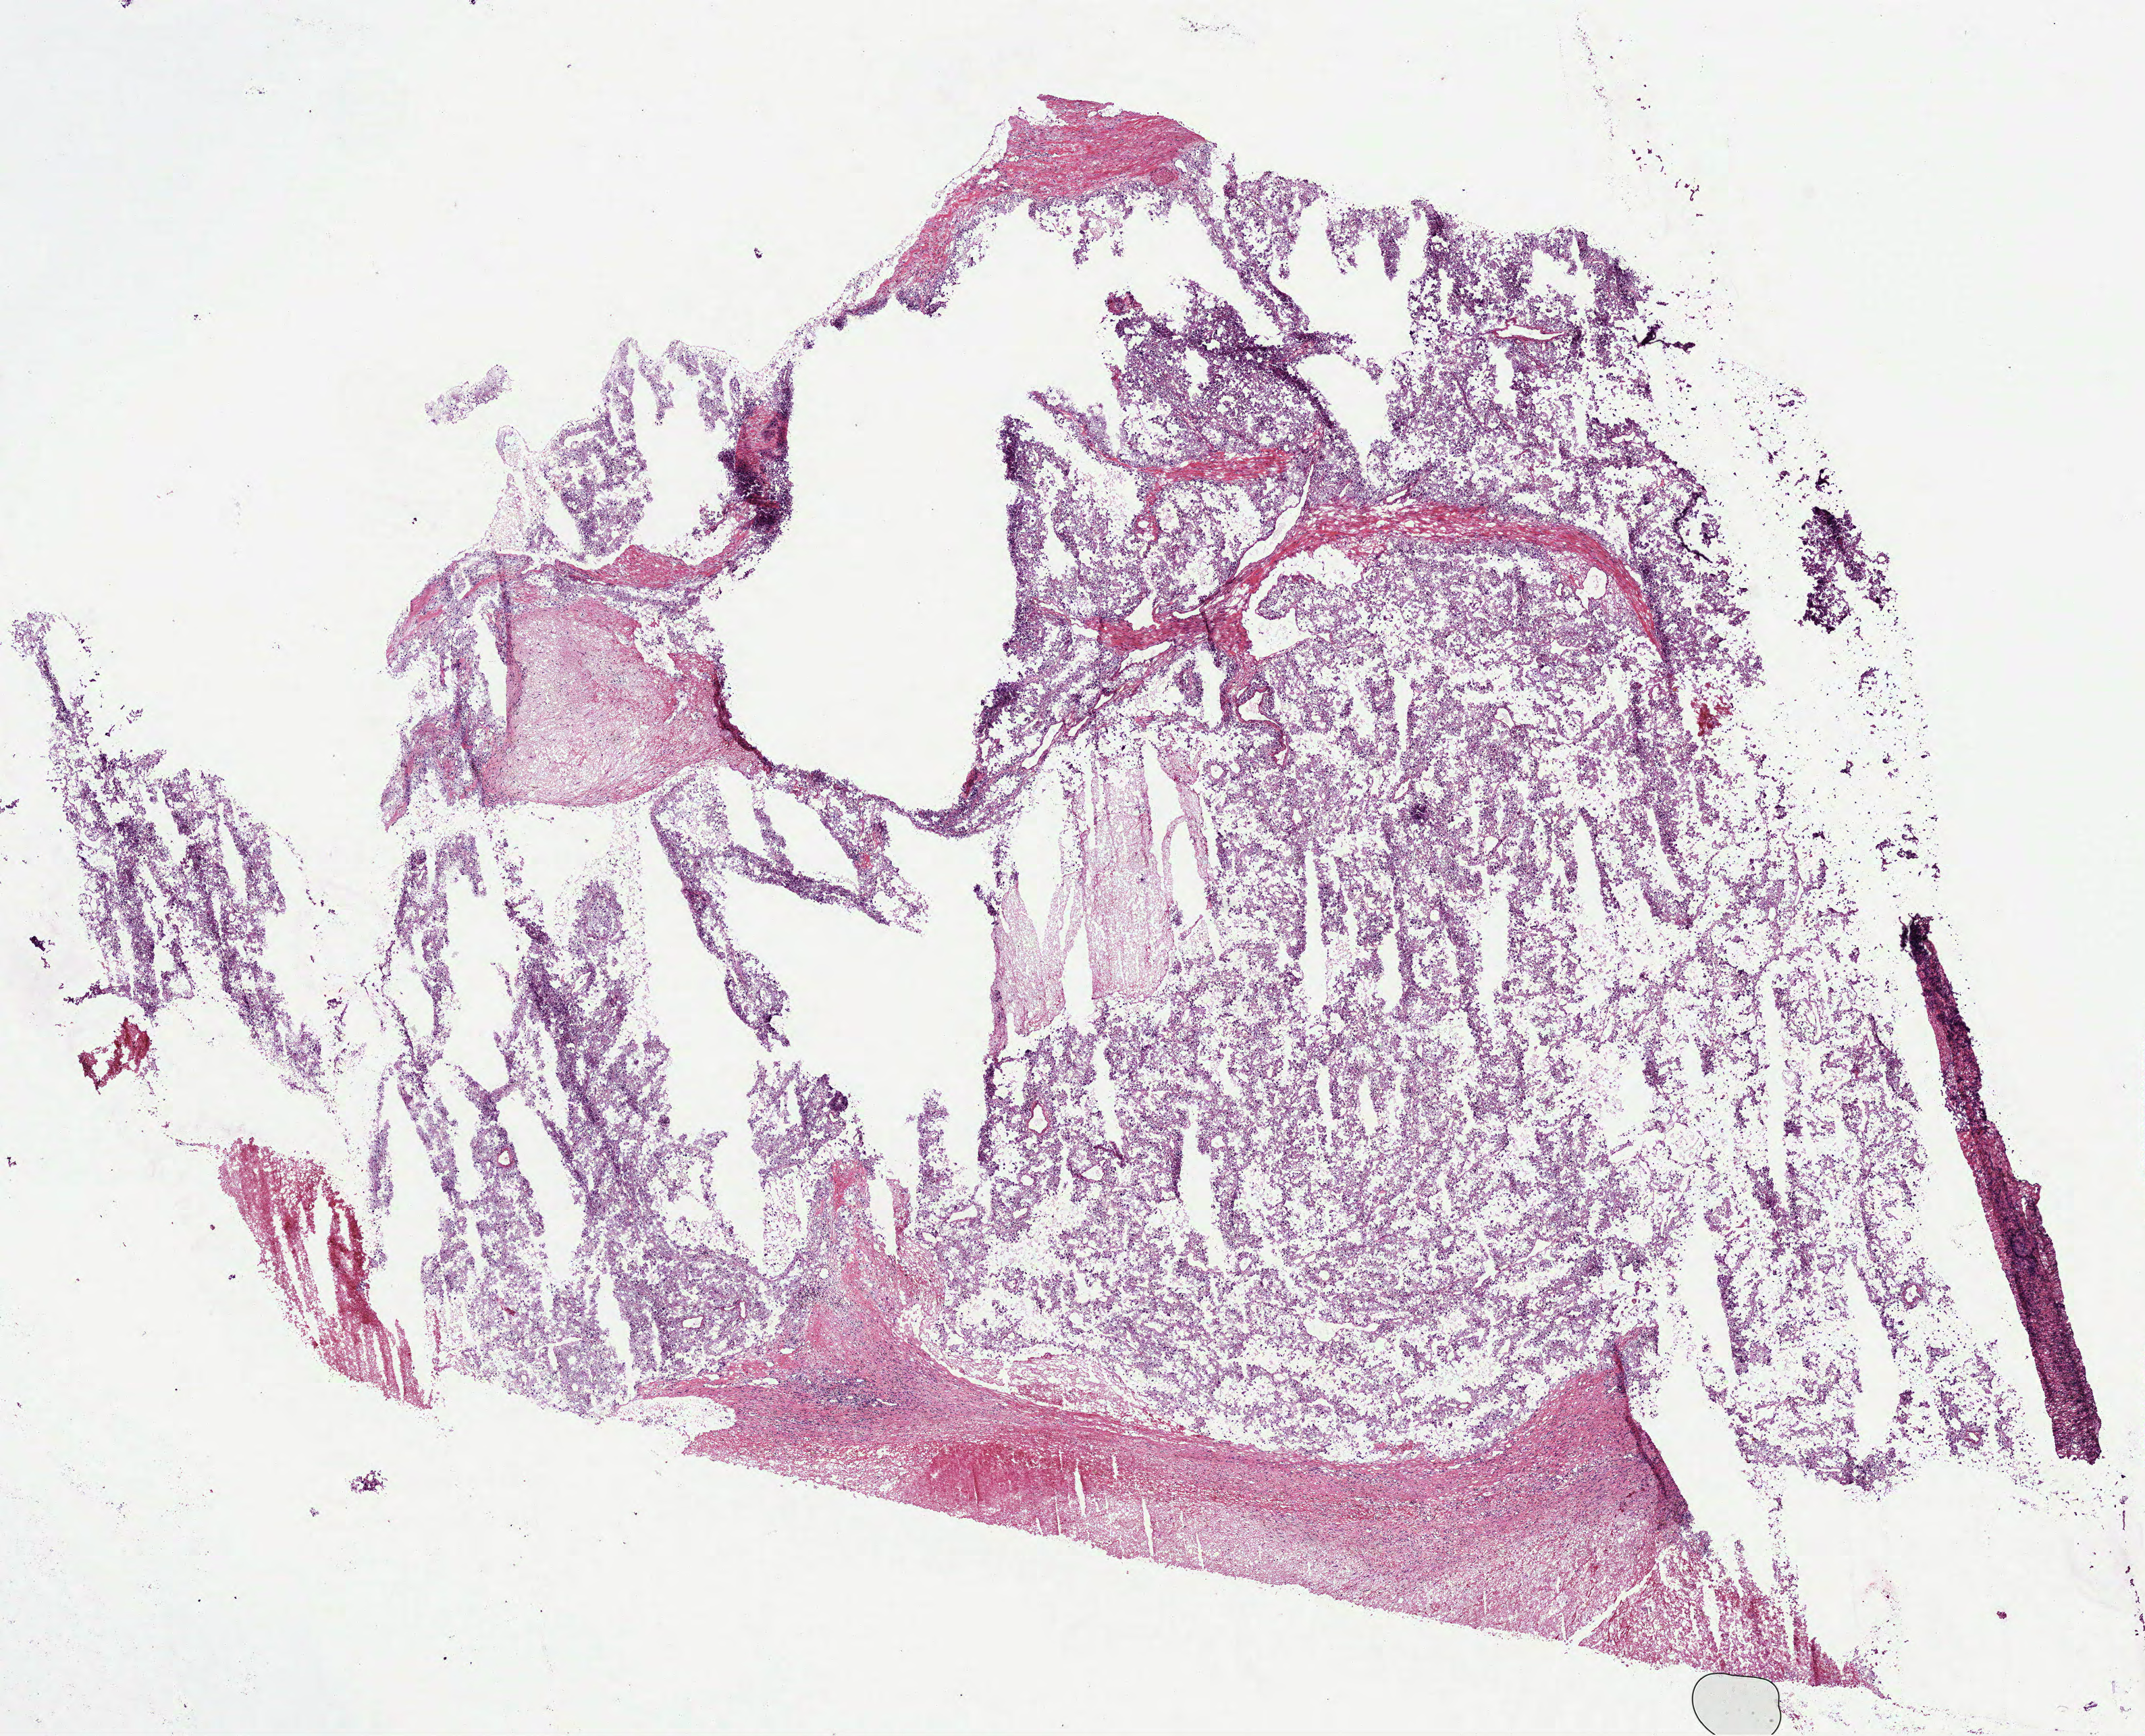
Hematoxylin and eosin (H&E) stained whole-slide image, a low-resolution overview of the entire scanned area, about 12.8 x 10.4 mm (acquisition: 40x scan); frozen section from the bottom of the tissue portion; kidney, primary tumour sample. Male patient; age at initial diagnosis 54 years. Composition of this section per pathologist review: tumour cells 83%, tumour nuclei 80%, normal cells 0%, stromal cells 15%, necrosis 2%.
* AJCC pathologic stage: III (6th edition)
* pathologic diagnosis: Papillary adenocarcinoma, NOS